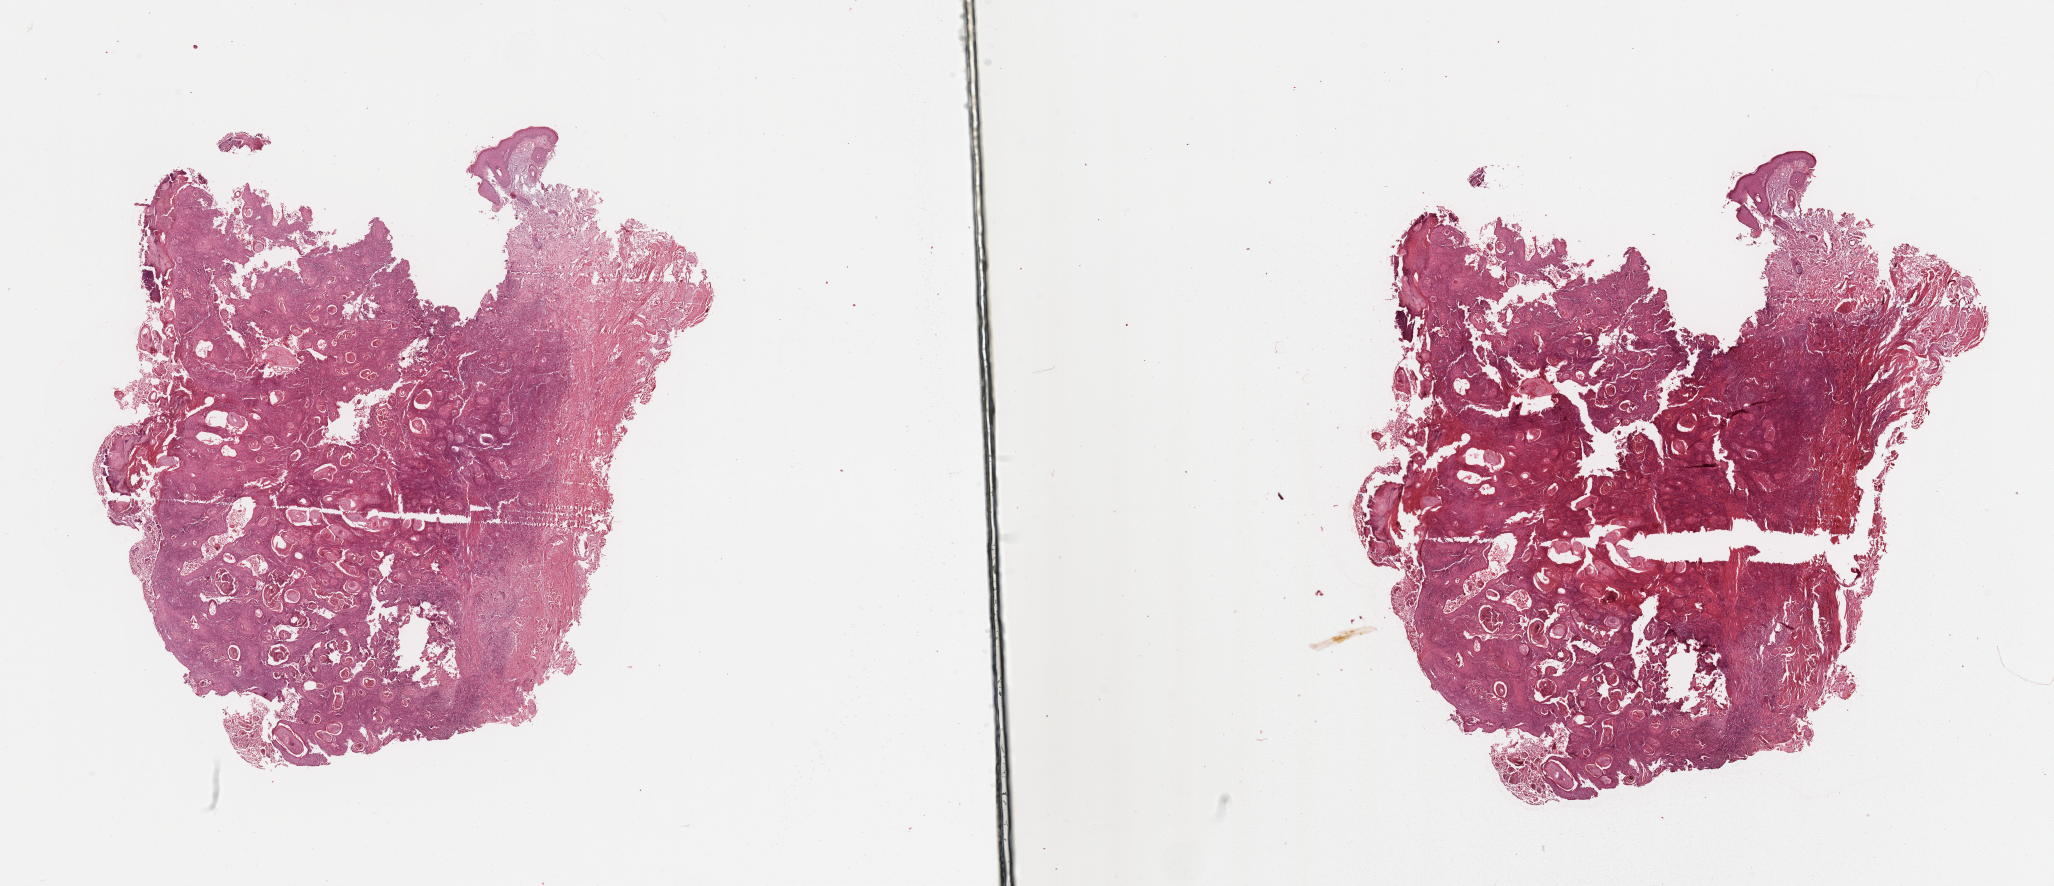
H&E-stained whole-slide image, low-resolution overview of the scanned area, about 32.5 x 14.0 mm. Tumour tissue sample, sampled site: lip. 80-year-old female patient. Histologic grade: G1 (well differentiated). Slide review estimates, as recorded: tumour nuclei 85%, necrosis 2%.
* AJCC pathologic stage: II
* primary tumour site (as recorded): lip
* histologic diagnosis: Squamous cell carcinoma, NOS (lip, NOS)